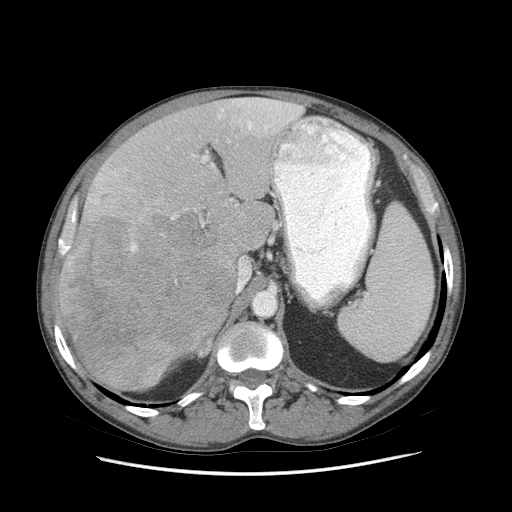
Contrast-enhanced abdominal CT (liver protocol), one axial slice; reconstruction kernel STANDARD; soft-tissue window (W 400 / L 40 HU); 512 × 512 image matrix. Case-level facts recorded for this patient, not image findings: diagnosis: hepatocellular carcinoma (patient treated with transarterial chemoembolisation; whether this scan precedes or follows treatment is not stated here); TNM stage (as recorded): Stage-IIIB; Child-Pugh class: A; tumour differentiation: moderately differentiated; tumour nodularity: multinodular.
Outlined on this slice (semi-automatically segmented with operator editing):
- liver parenchyma outside the tumour (the mass and vessels are separate outlines, so this box may not span the whole liver): bounding box [x1, y1, x2, y2] px = [56, 98, 302, 390]
- mass: [60, 209, 237, 390]
- liver vessels: [63, 98, 300, 254]